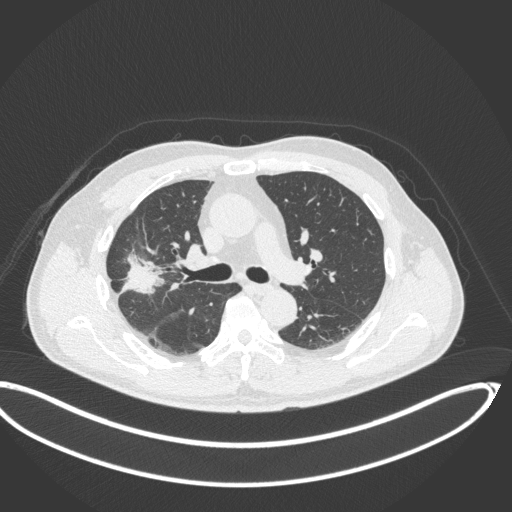
Chest CT, one axial slice; position 214 of 341 along the scan axis; reconstruction kernel B31f; 120 kVp; lung window (W 1500 / L -600 HU); 1 mm slice thickness; 512 × 512 image matrix, field of view 439 × 439 mm. Male patient, age 63 years. Case-level facts recorded for this patient, not image findings: clinical TNM (as recorded): T1c N0 M0; histopathological grade: G2-3.
Structures marked on this image (bounding box drawn by a radiologist):
- lung tumour (recorded histology: adenocarcinoma): box from (x=119, y=251) to (x=164, y=299) px